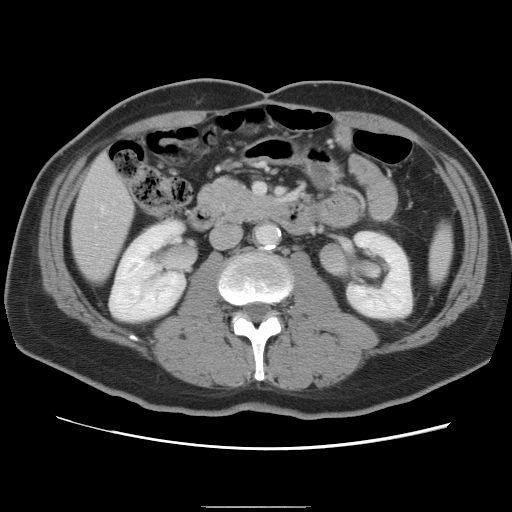
Contrast-enhanced abdominal CT, one axial slice; slice 26 of 87 in the series (ordered by position); 120 kVp; intravenous contrast given; soft-tissue window (W 400 / L 40 HU); 5 mm slice thickness; 512 × 512 image matrix. Male patient, age 63 years. Case-level facts recorded for this patient, not image findings: diagnosis: colorectal cancer liver metastases, imaged before liver resection; multiple liver metastases: no; largest metastasis: 9 cm.
Structures marked on this image (manually delineated by an expert):
- liver: bounding box [x1, y1, x2, y2] px = [73, 157, 135, 280]
- planned liver remnant (the part of the liver to remain after resection): [73, 157, 134, 280]